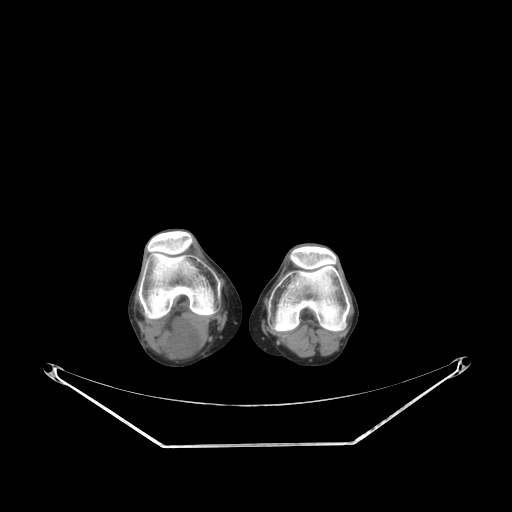
CT of an extremity soft-tissue mass (from a PET/CT study), one axial slice. 140 kVp. Soft-tissue window (W 400 / L 40 HU). 3.75 mm slice thickness. 512 × 512 image matrix, field of view 500 × 500 mm. Female patient. Case-level facts recorded for this patient, not image findings: histological type: liposarcoma; site of the primary tumour: right thigh.
Annotated regions visible in this slice (expert contour drawn on MRI and transferred to this co-registered scan by the dataset authors):
- gross tumour volume (mass): box from (x=157, y=314) to (x=200, y=357) px